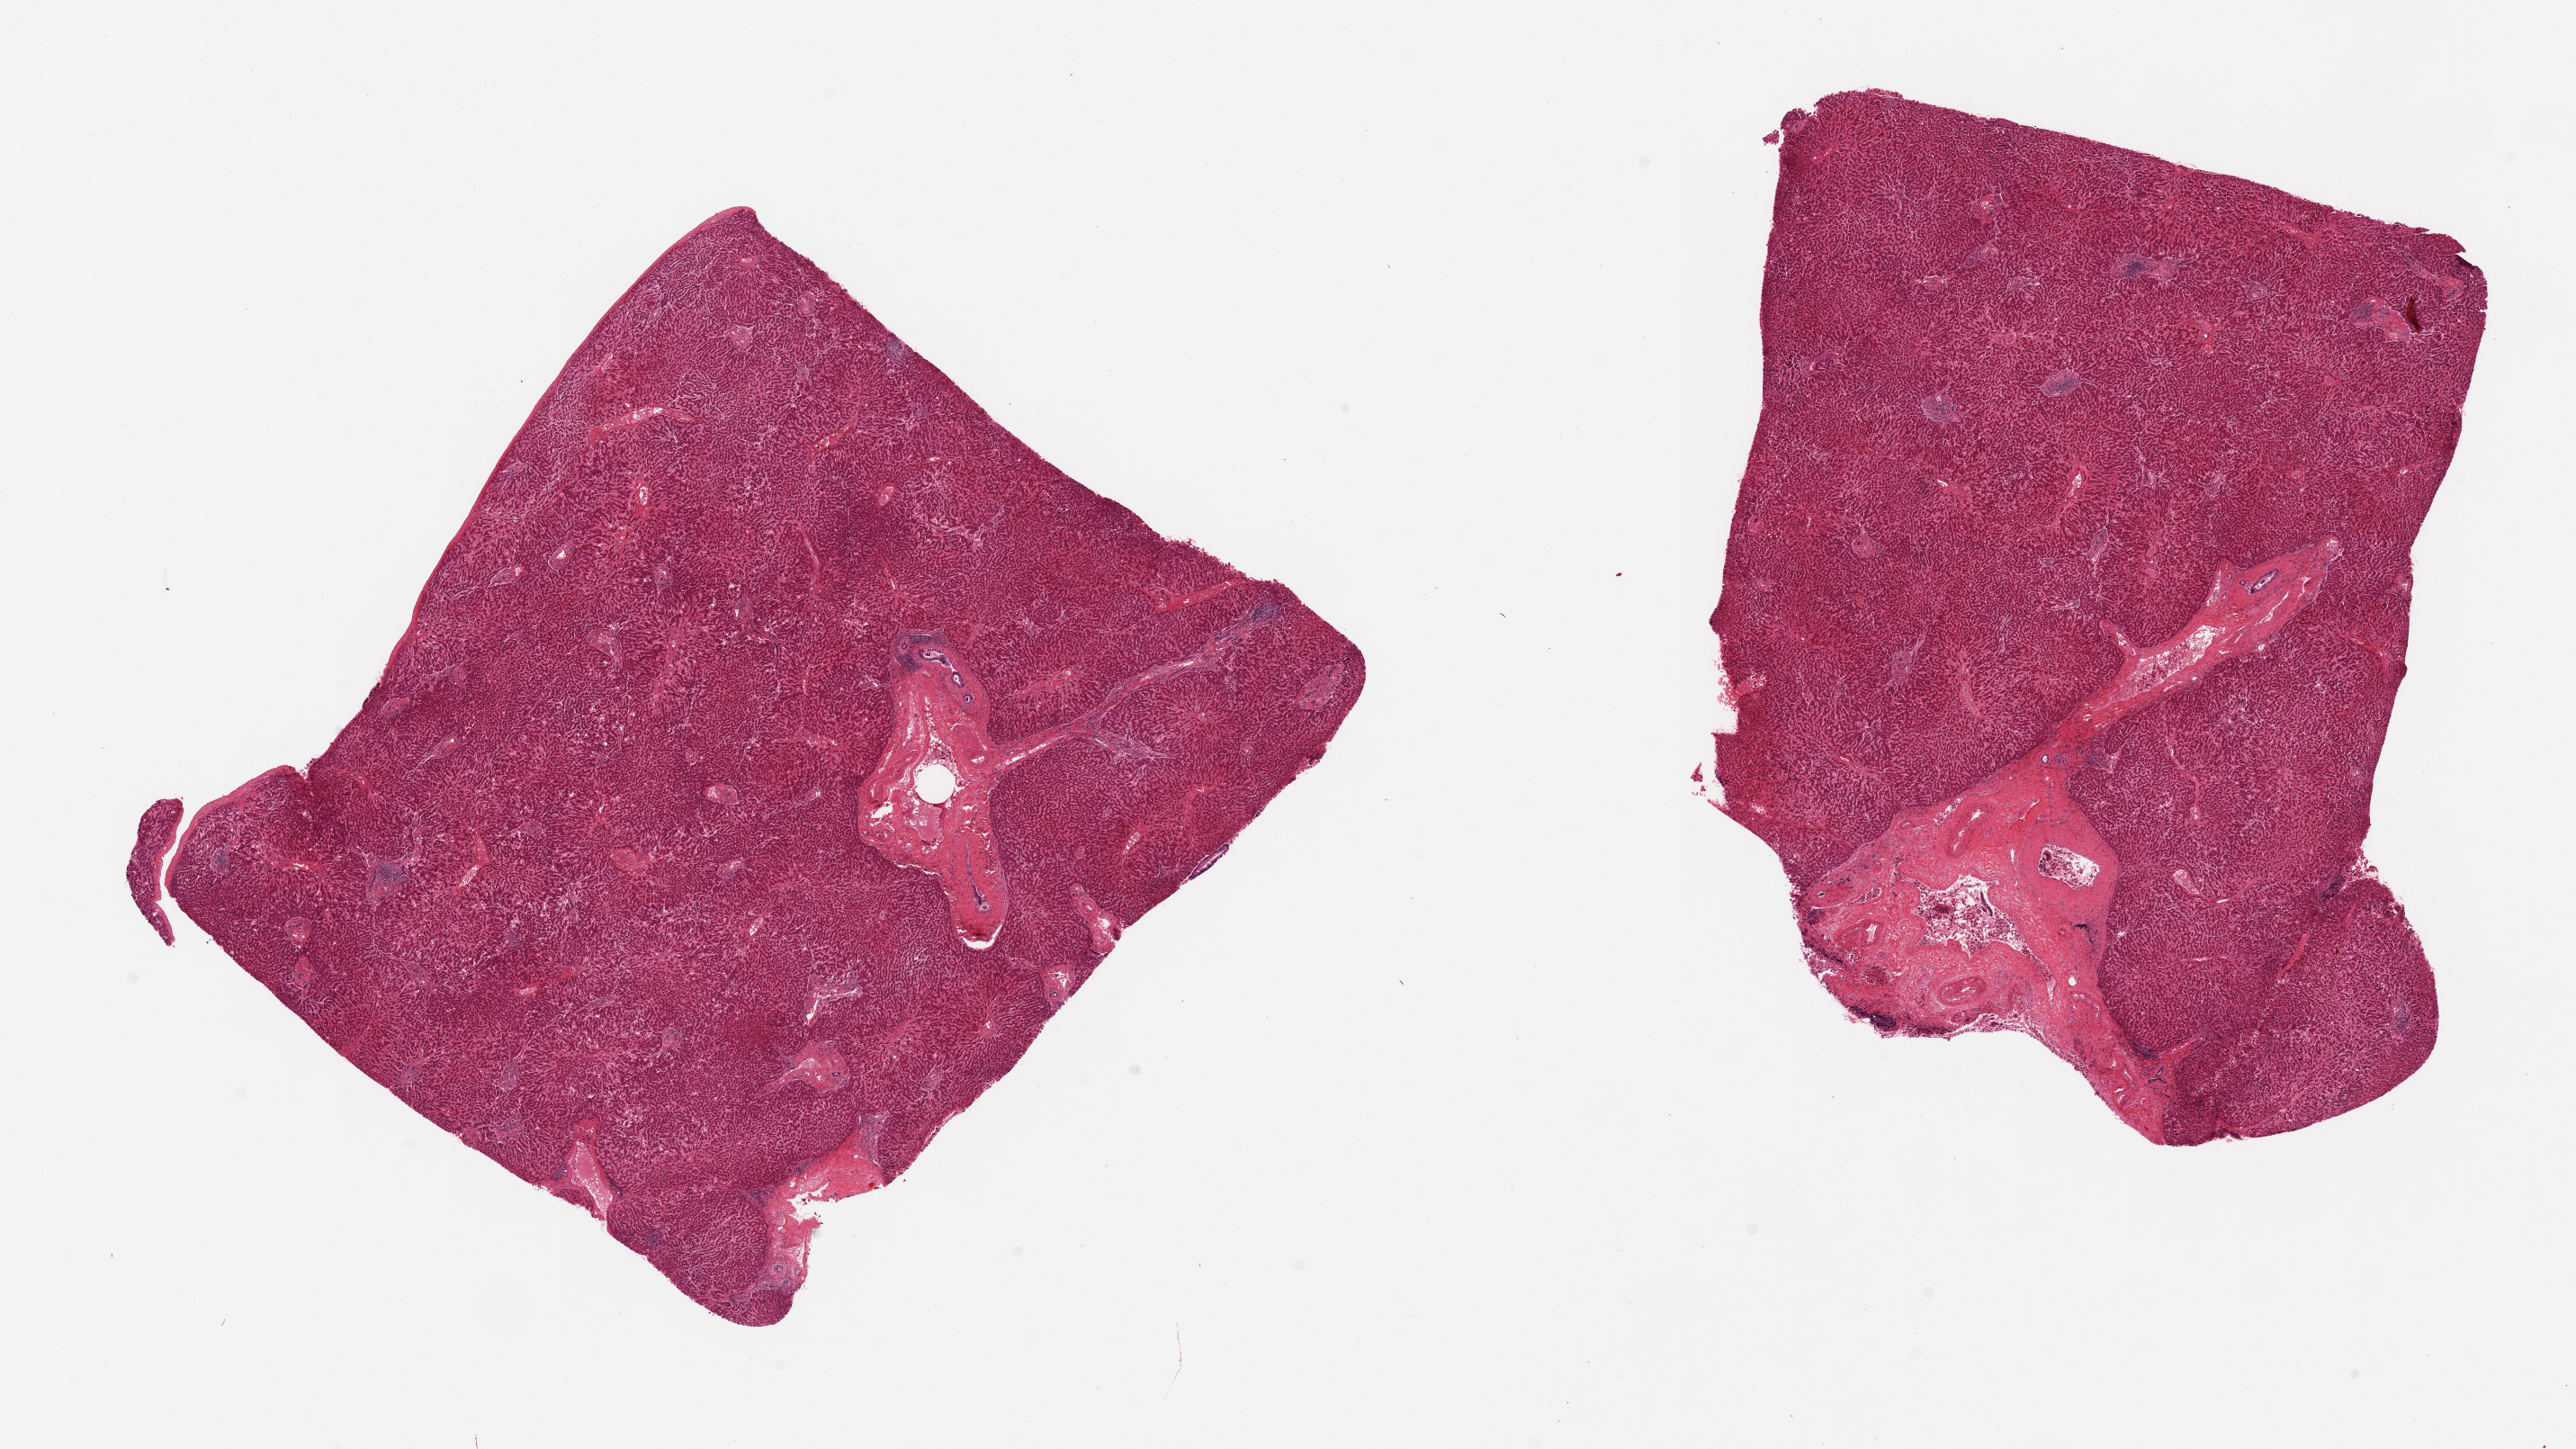
Hematoxylin and eosin (H&E) whole-slide image — whole scanned area (about 22.6 x 12.7 mm, slide scanned at 20x) shown as a low-resolution overview; PAXgene-fixed, paraffin-embedded tissue; sampled site (target tissue): liver; tissue donor sample. Donor sex: female.
Review note (as recorded): 2 pieces ~7x7mm, moderately-badly autolyzed, prominent fibrous areas.